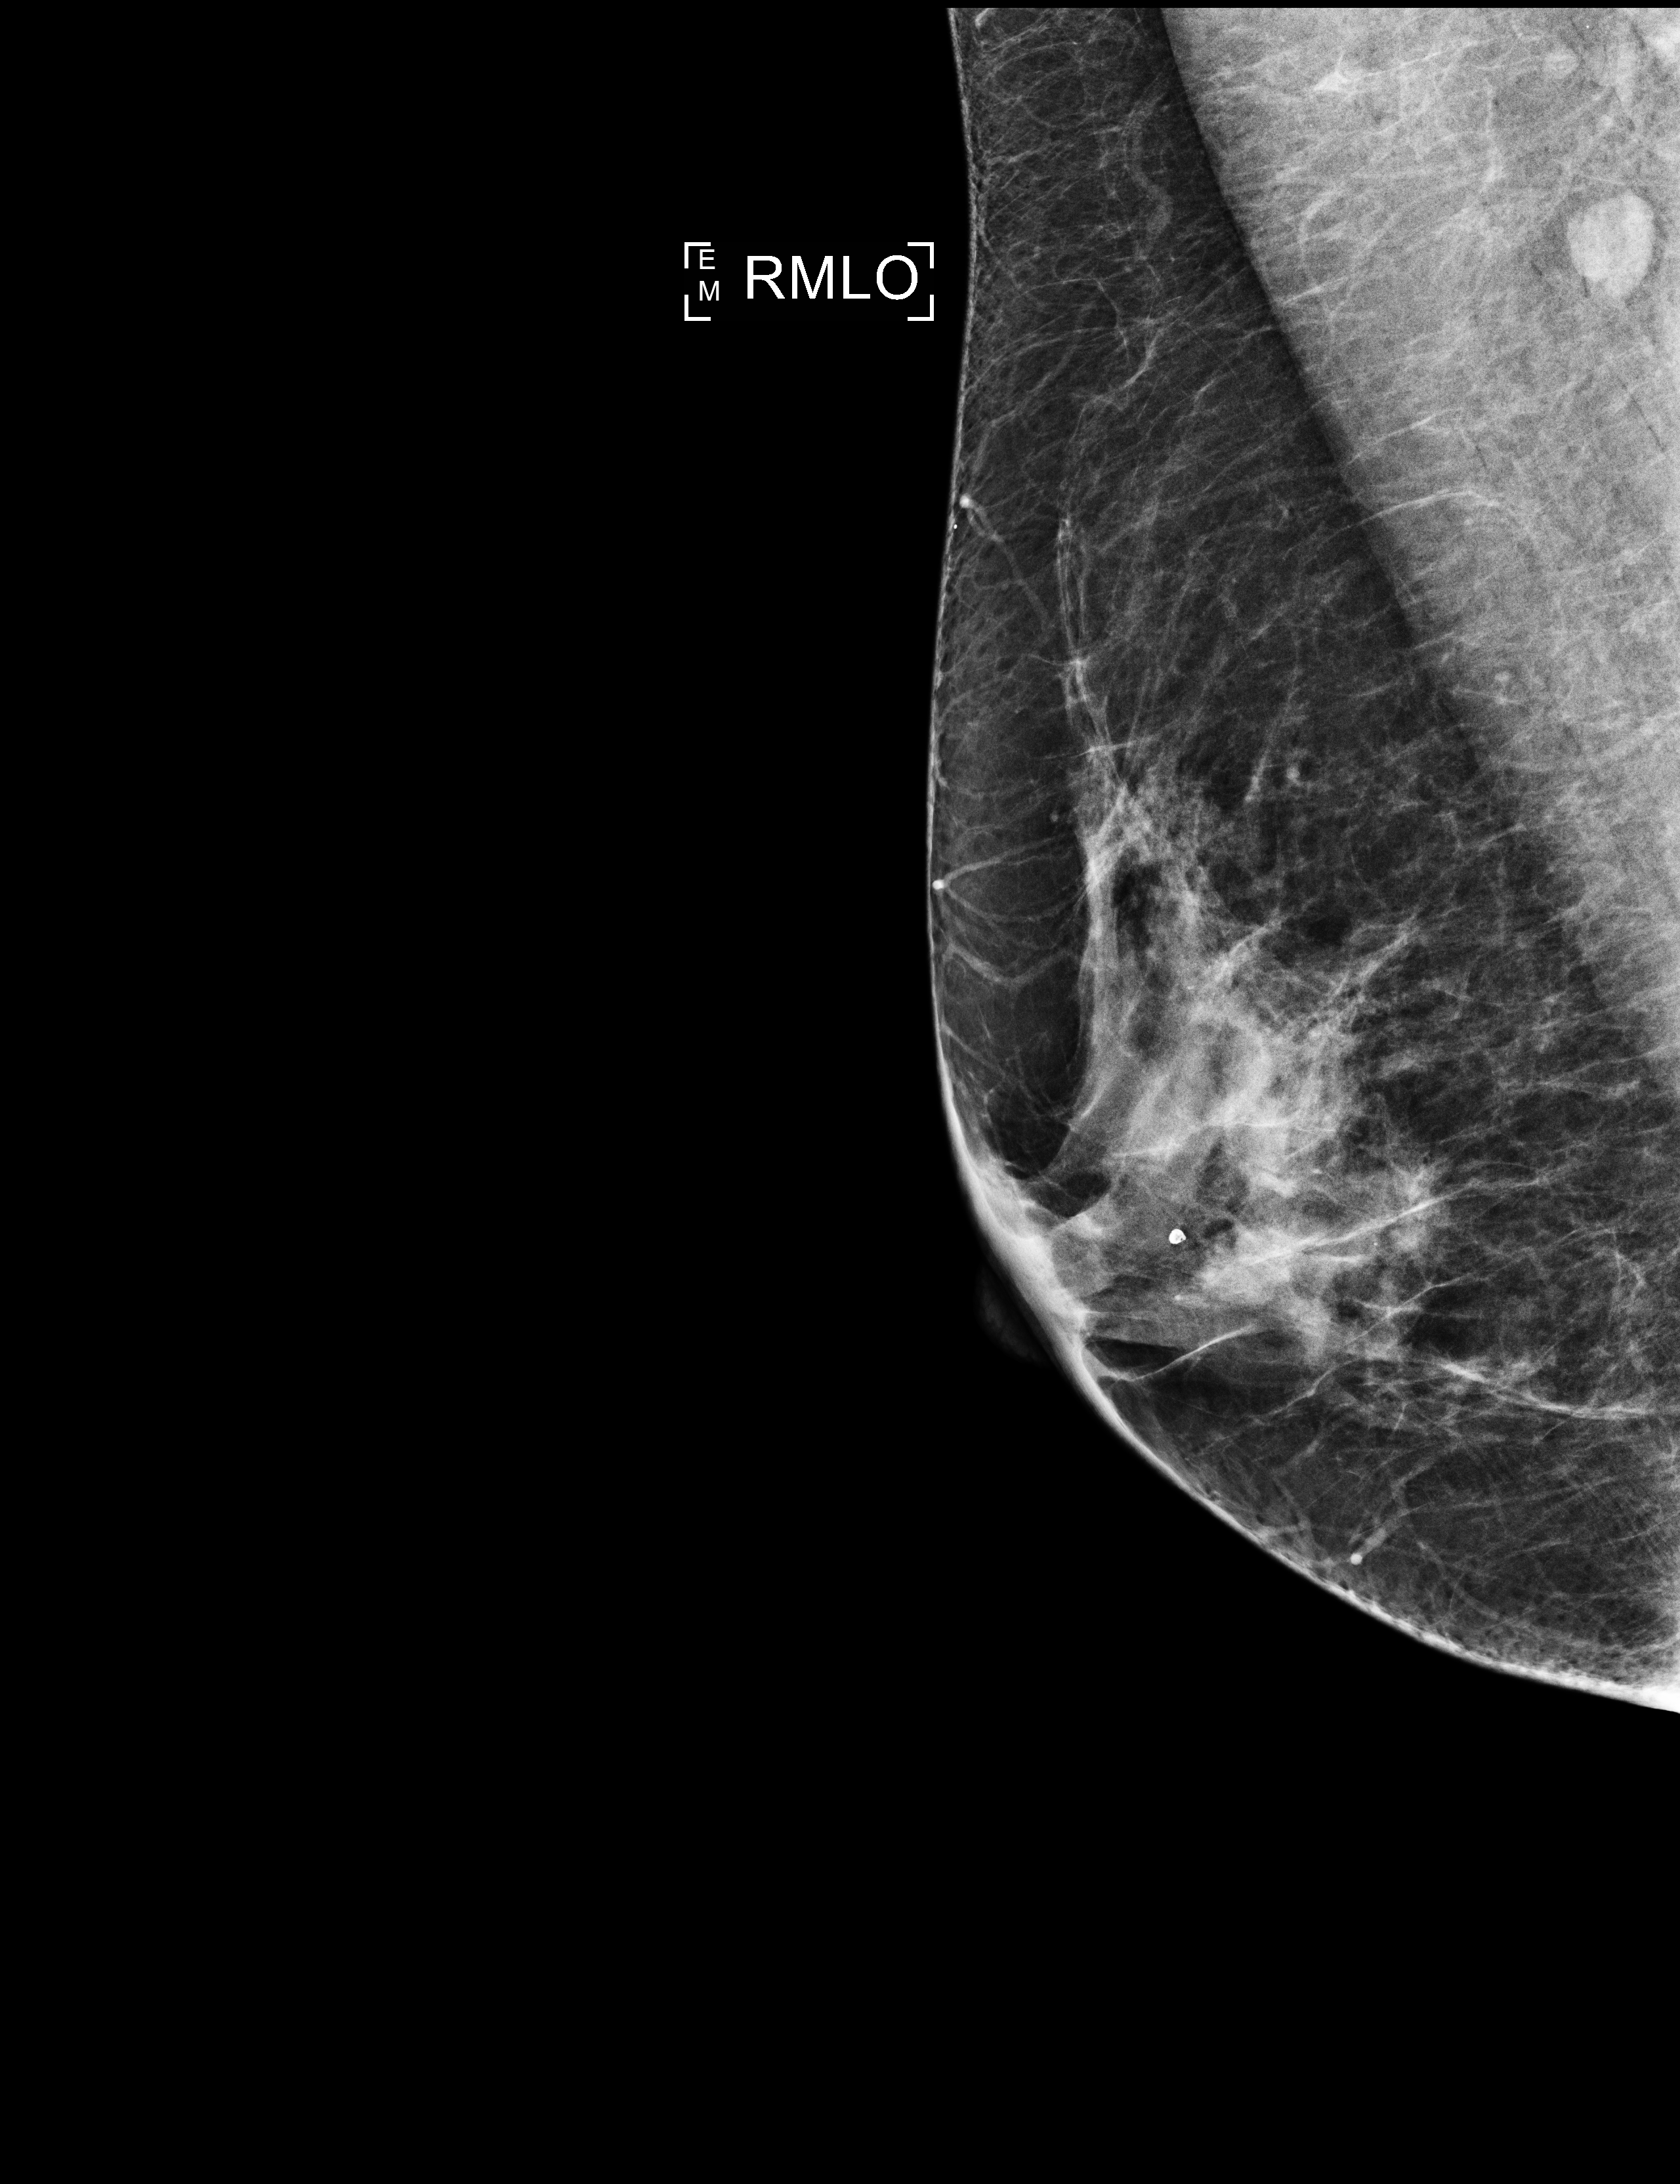
Full-field digital mammogram (FFDM), right breast, MLO view, screening examination, compressed breast thickness 54 mm, system: Selenia Dimensions. Female patient, age 56 years.
BI-RADS breast density category at the screening exam (both breasts, scale 1–4): 3. Final BI-RADS category for the screening round (tomosynthesis exam, both breasts): category 2. Recall: no recall after this screen.